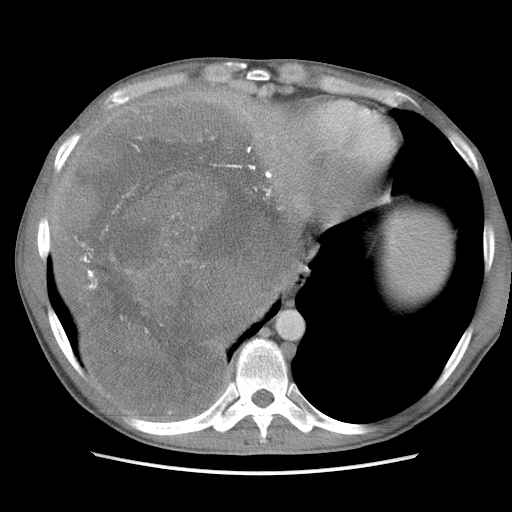
Contrast-enhanced abdominal CT, one axial slice; position 90 of 115 along the scan axis; soft-tissue window (W 400 / L 40 HU); 512 × 512 image matrix, field of view 360 × 360 mm. Male patient. From the clinical record (not read from this slice): diagnosis: adrenocortical carcinoma; tumour side: right adrenal.
Annotated regions visible in this slice (semi-automatically segmented with operator editing):
- mass: bounding box <62,103,296,417> (left, top, right, bottom; pixels)